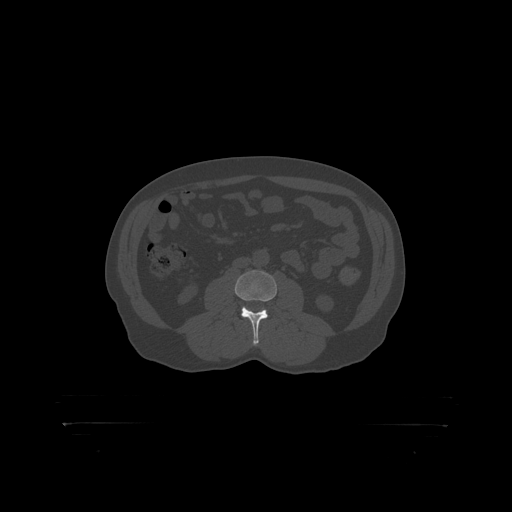
CT including the spine, one axial slice. Slice 261 of 399 in the series (ordered by position). Reconstruction kernel STANDARD. Bone window (W 1800 / L 400 HU). 1.25 mm slice thickness. 512 × 512 image matrix. Patient: male, 46 years. From the clinical record (not read from this slice): primary cancer: skin.
Outlined on this slice (semi-automatically segmented with operator editing):
- L3 vertebra: bounding box [x1, y1, x2, y2] px = [235, 271, 278, 319]